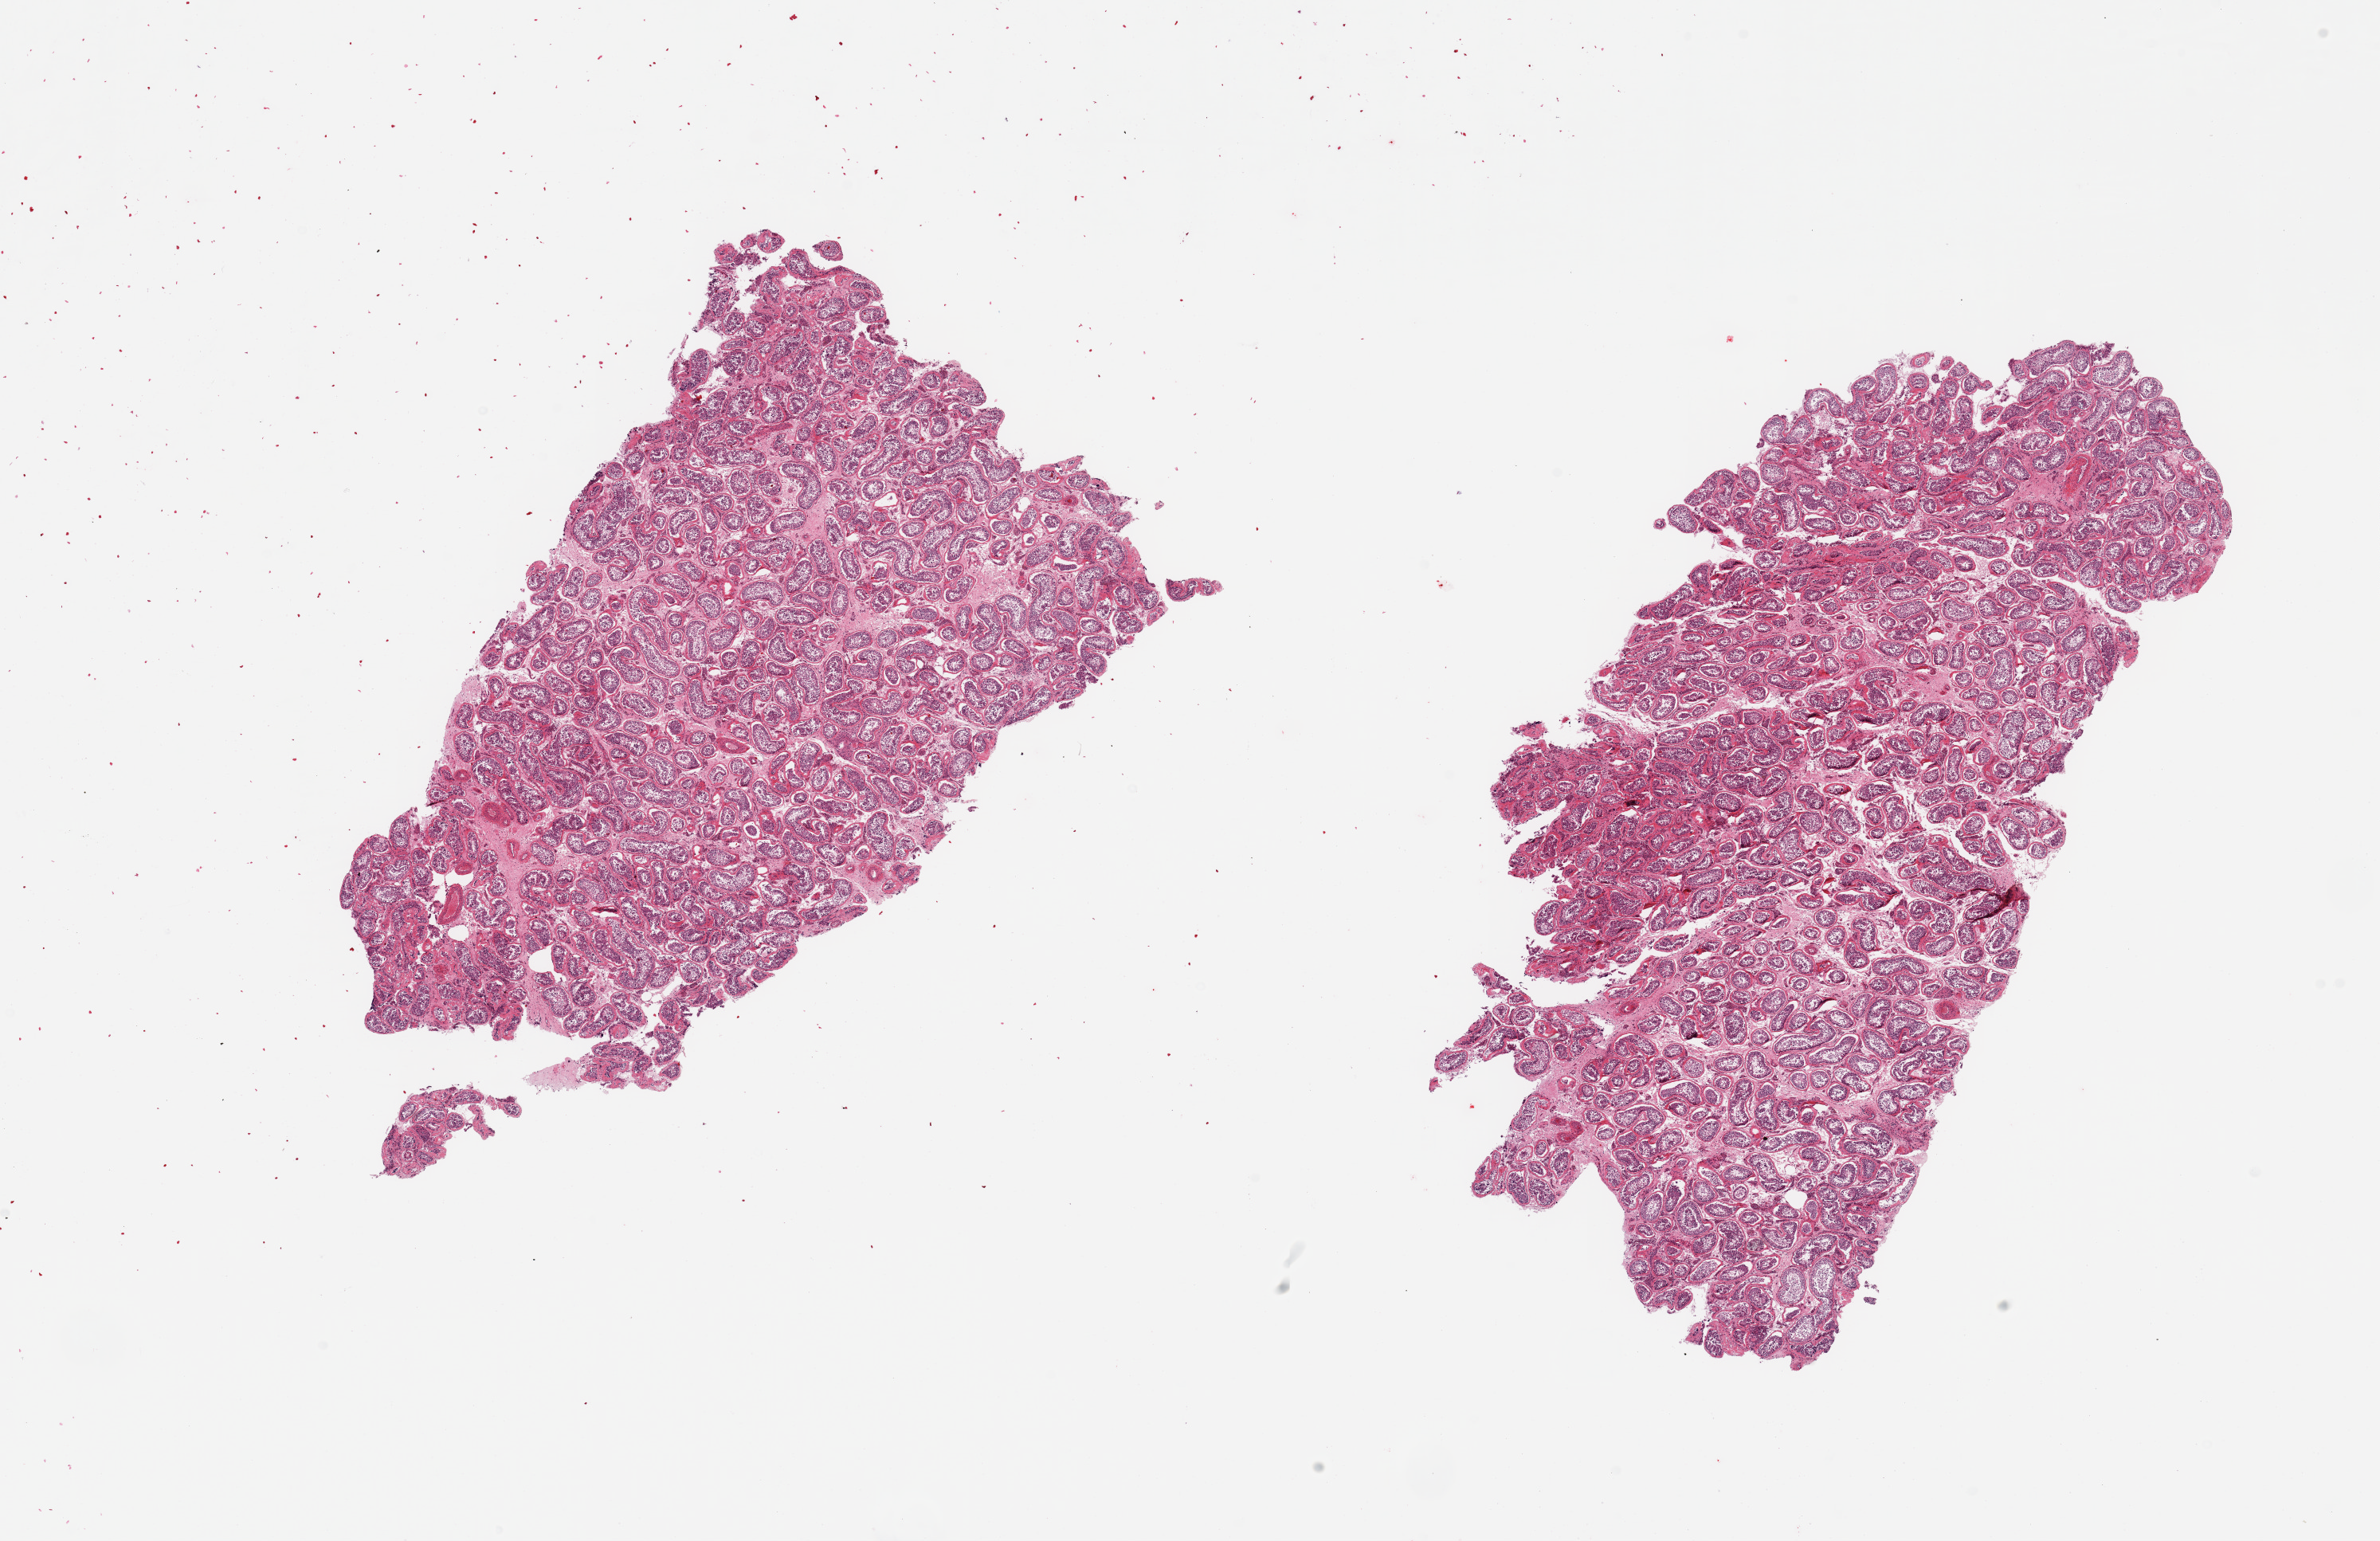
Whole-slide image, H&E stain, whole scanned area (about 23.6 x 15.3 mm) shown as a low-resolution overview. PAXgene-fixed paraffin-embedded (PFPE) section. Section of testis (target tissue). Tissue donor sample. Donor: male.
Pathologist's review note for this sample: 2 pieces; spermatogenesis is present.